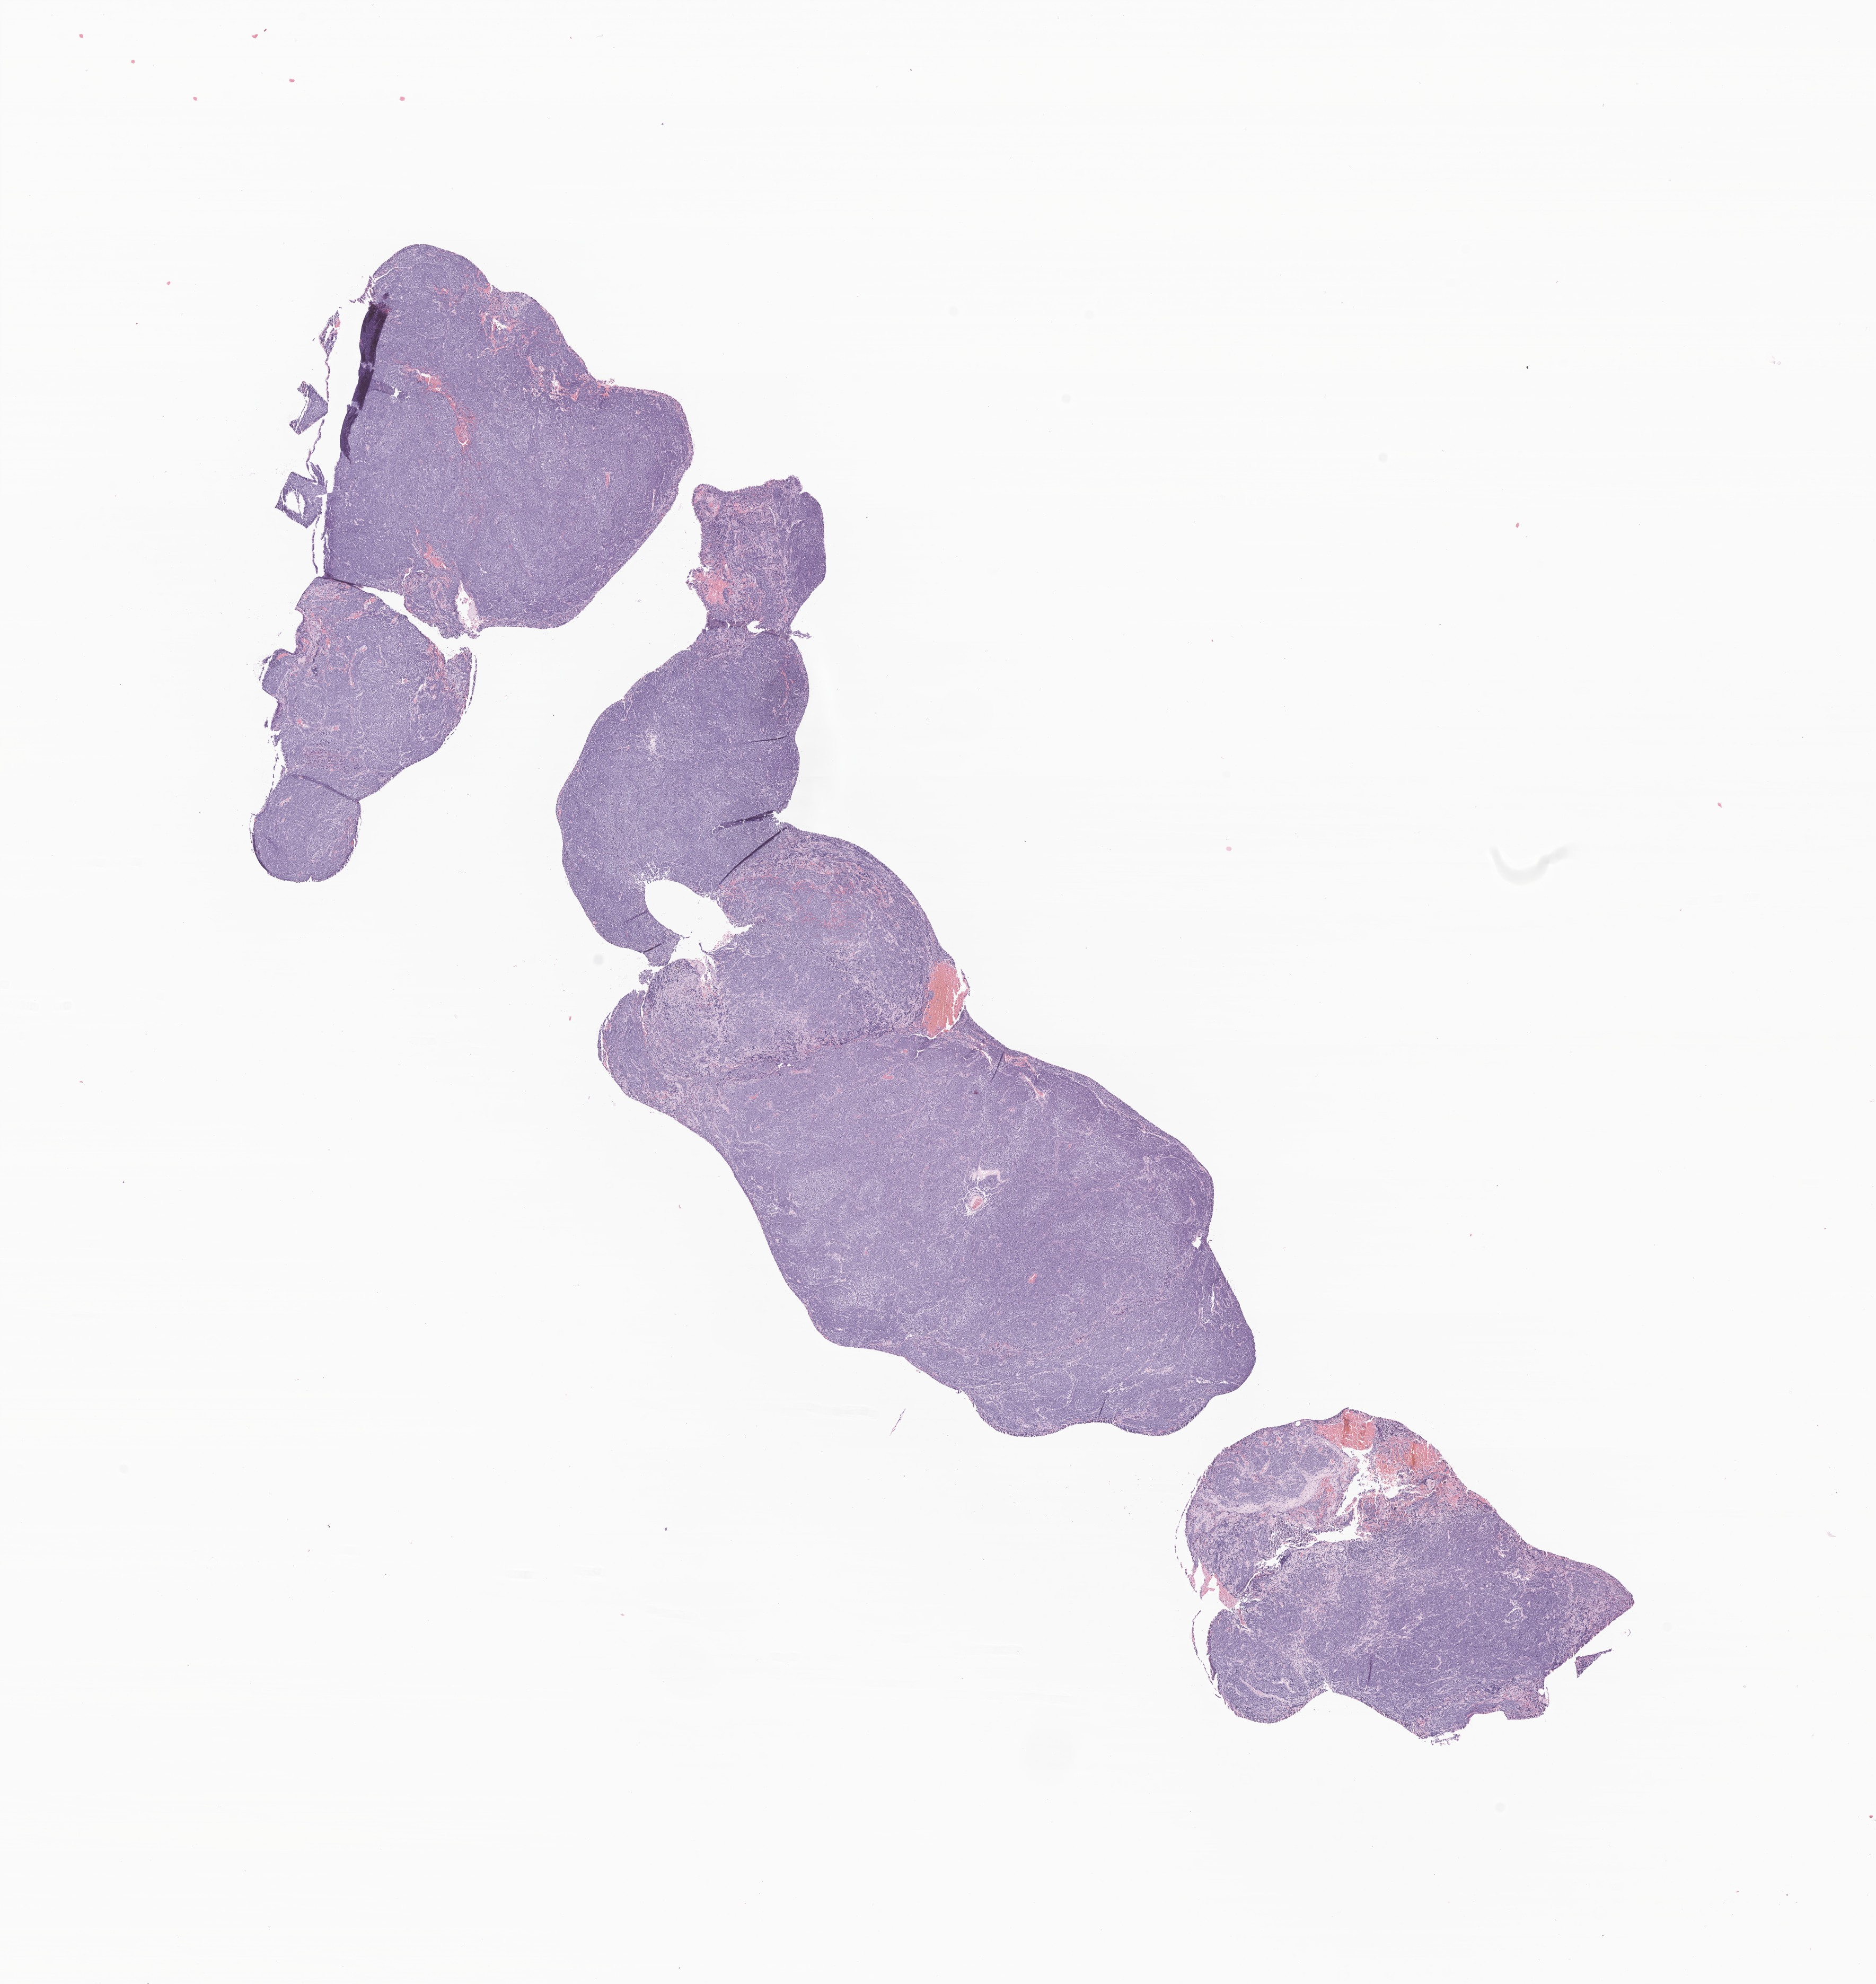
Digitized haematoxylin and eosin-stained section of tumor tissue from the cerebellum — low-resolution overview of the scanned area, about 14.9 x 15.8 mm; formalin-fixed, paraffin-embedded (FFPE) tissue. Patient female; age 181 months (15 years 1 month).
Recorded diagnosis: Medulloblastoma, NOS.